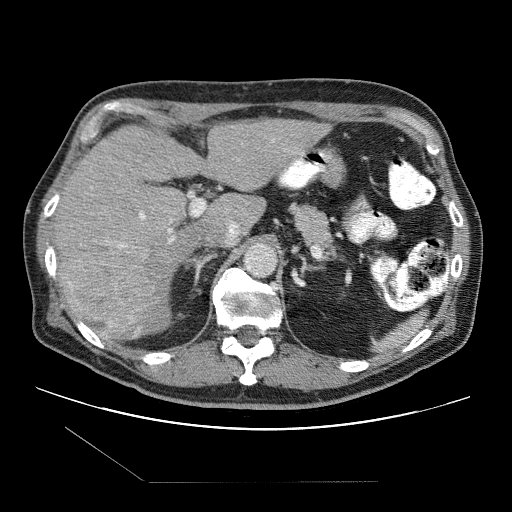
Contrast-enhanced abdominal CT (liver protocol), one axial slice. Slice 60 of 109 in the series (ordered by position). 120 kVp. One of 2 acquisitions stored at this slice position. Soft-tissue window (W 400 / L 40 HU). 2.5 mm slice thickness. 512 × 512 image matrix. Case-level facts recorded for this patient, not image findings: diagnosis: hepatocellular carcinoma (patient treated with transarterial chemoembolisation; whether this scan precedes or follows treatment is not stated here); TNM stage (as recorded): Stage-IIIB; Child-Pugh class: A; tumour differentiation: well differentiated.
Outlined on this slice (semi-automatic segmentation, software-assisted and operator-edited):
- liver parenchyma outside the tumour (the mass and vessels are separate outlines, so this box may not span the whole liver): bounding box <54,118,328,336> (left, top, right, bottom; pixels)
- mass: <60,237,159,331>
- liver vessels: <139,211,175,243>